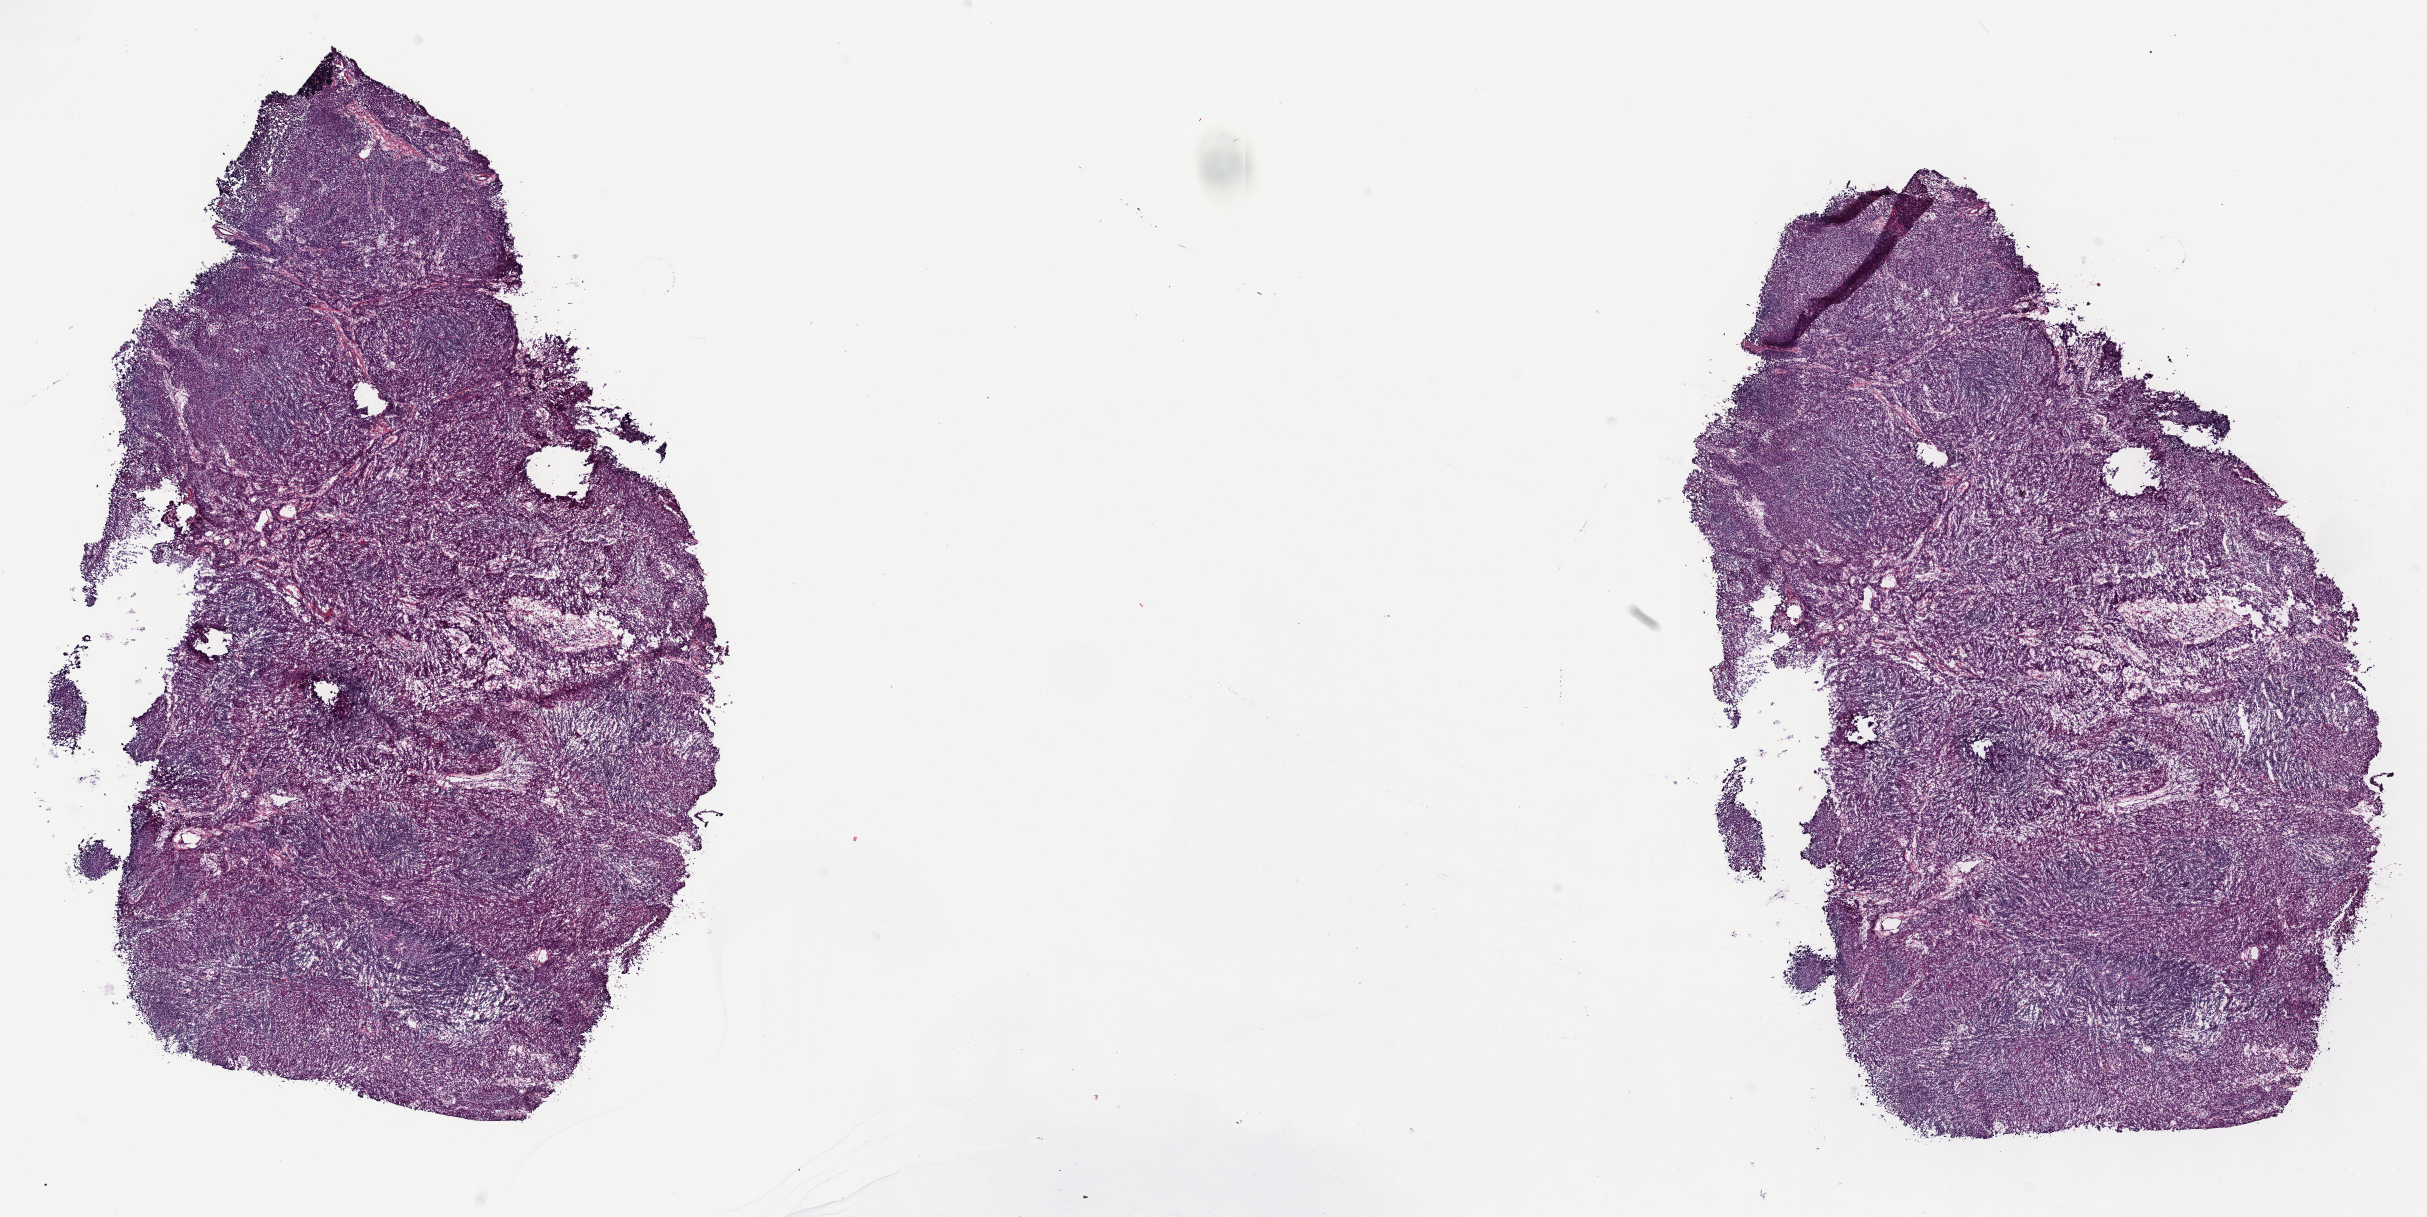
Whole-slide histology image, H&E-stained, whole scanned area (about 19.6 x 9.8 mm, from a 40x scan) shown as a low-resolution overview, frozen section, sample: primary tumour, thymus. Female patient; age at initial diagnosis 52 years. Slide review estimates, as recorded: tumour cells 99%, tumour nuclei 99%, normal cells 0%, stromal cells 1%, necrosis 0%. Infiltration values recorded for this section: lymphocyte infiltration 0%, monocyte infiltration 0%, neutrophil infiltration 0%.
- histologic diagnosis: Thymic carcinoma, NOS